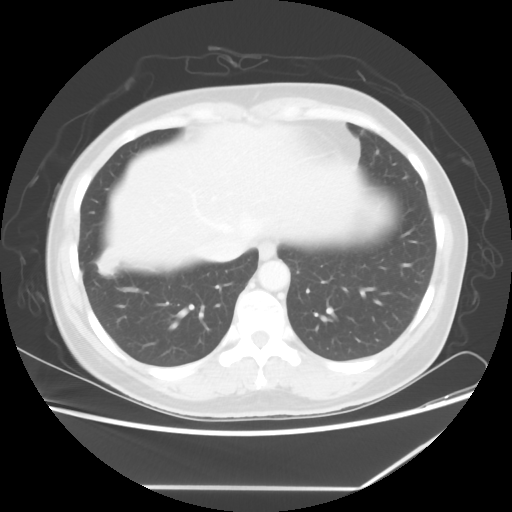
Chest CT, one axial slice; 100 kVp; lung window (W 1500 / L -600 HU); 5 mm slice thickness; 512 × 512 image matrix. Female patient, age 42 years. From the clinical record (not read from this slice): clinical TNM (as recorded): T2 N1 M0.
Annotated regions visible in this slice (rectangle marked by the reading radiologist):
- lung tumour (recorded histology: adenocarcinoma): bounding box (x1, y1, x2, y2) in pixels: (95, 241, 117, 280)